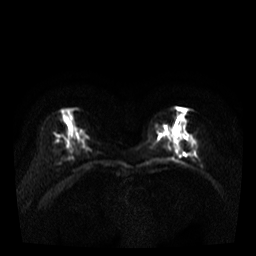
Breast MRI, one axial slice; slice 13 of 35 in the series (ordered by position); diffusion-weighted series; image 2 of 4 stored at this slice position (different b-values; order by instance number); 3 T; 5 mm slice thickness; 256 × 256 image matrix, field of view 320 × 320 mm. Female patient.
Structures marked on this image (expert manual segmentation):
- tumour on diffusion-weighted imaging: bounding box <175,145,178,149> (left, top, right, bottom; pixels)